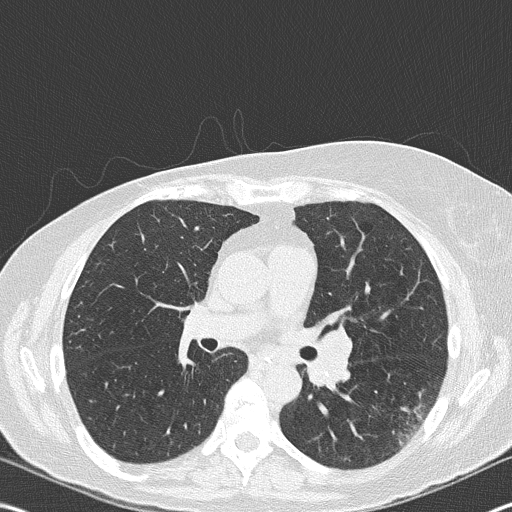
Low-dose screening chest CT, one axial slice. Slice 102 of 177 in the series (ordered by position). Lung window (W 1500 / L -600 HU). 512 × 512 image matrix, field of view 342 × 342 mm.
Outlined on this slice (outlined manually by an expert reader):
- lesion 1 (tumor): bounding box (x1, y1, x2, y2) in pixels: (405, 408, 420, 418)
- lesion 2 (nodule, hilum of left lung): (304, 326, 353, 389)